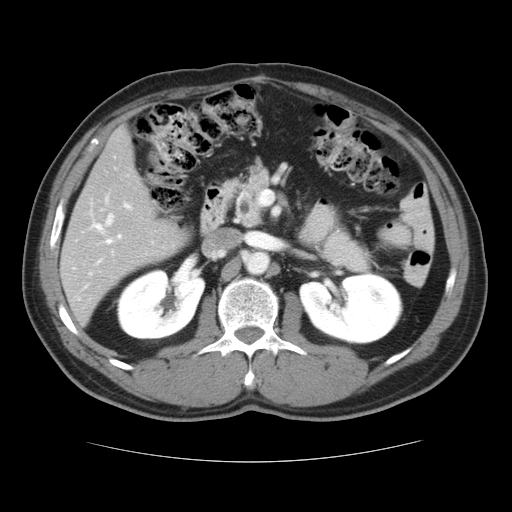
Contrast-enhanced abdominal CT, one axial slice. Slice 17 of 37 in the series (ordered by position). 120 kVp. Intravenous contrast given. Soft-tissue window (W 400 / L 40 HU). 512 × 512 image matrix. Male patient, age 66 years. From the clinical record (not read from this slice): diagnosis: colorectal cancer liver metastases, imaged before liver resection; multiple liver metastases: yes; largest metastasis: 1.6 cm; disease in both lobes: yes.
Annotated regions visible in this slice (outlined manually by an expert reader):
- hepatic veins: box from (x=105, y=195) to (x=115, y=227) px
- liver: (x=60, y=130)–(x=190, y=324)
- planned liver remnant (the part of the liver to remain after resection): (x=60, y=198)–(x=190, y=324)
- portal vein (with intrahepatic branches): (x=93, y=203)–(x=131, y=262)